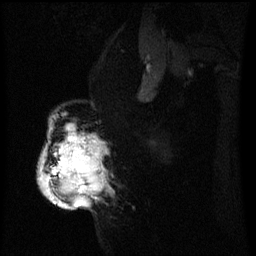
Breast MRI (dynamic contrast-enhanced), one sagittal slice; slice 41 of 60 in the series (ordered by position); dynamic contrast-enhanced series, image 2 of 3 at this slice position (ordered by acquisition); 1.5 T; TE 4.2 ms, TR 8 ms; 2.2 mm slice thickness; 256 × 256 image matrix. Patient: female, 50 years.
Structures marked on this image (semi-automatic segmentation, software-assisted and operator-edited):
- analysis volume of interest (the breast-tissue region the enhancement analysis was run in; not a lesion): bounding box [x1, y1, x2, y2] px = [38, 124, 105, 209]
- tumour enhancement mask (voxels above the 70 % enhancement threshold inside the analysis volume of interest): [40, 132, 105, 209]